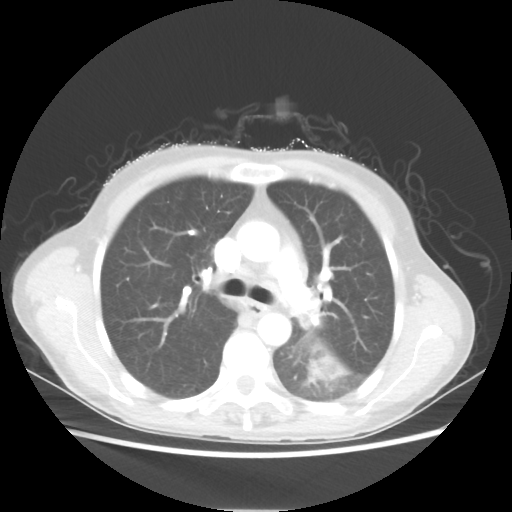
Chest CT, one axial slice. Slice 36 of 56 in the series (ordered by position). Reconstruction kernel STANDARD. Lung window (W 1500 / L -600 HU). 5 mm slice thickness. 512 × 512 image matrix. Female patient, age 53 years. Case-level facts recorded for this patient, not image findings: clinical TNM (as recorded): T3 N0 M0.
Outlined on this slice (rectangle marked by the reading radiologist):
- lung tumour (recorded histology: adenocarcinoma): bounding box [x1, y1, x2, y2] px = [310, 356, 345, 385]